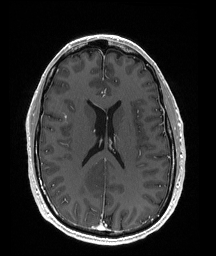
Brain MRI from a brain-tumour surgery series, one axial slice. Slice 78 of 176 in the series (ordered by position). T1-weighted post-contrast. 1 mm slice thickness. 216 × 256 image matrix. From the clinical record (not read from this slice): histopathology: Oligodendroglioma; WHO grade: 2.
Structures marked on this image (manually delineated by an expert):
- tumour: bounding box (x1, y1, x2, y2) in pixels: (85, 166, 107, 195)